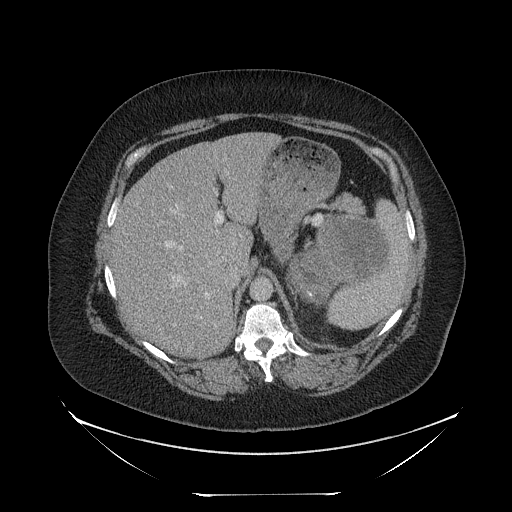
Contrast-enhanced abdominal CT, one axial slice. Position 163 of 205 along the scan axis. Reconstruction kernel STANDARD. 120 kVp. Intravenous contrast given. Soft-tissue window (W 400 / L 40 HU). 2.5 mm slice thickness. 512 × 512 image matrix. Female patient, age 53 years. Case-level facts recorded for this patient, not image findings: diagnosis: adrenocortical carcinoma; tumour side: left adrenal; tumour size at pathology: 17 cm; Ki-67 index: 20 %; stage (as recorded): 3.
Annotated regions visible in this slice (semi-automatically segmented with operator editing):
- mass: bounding box [x1, y1, x2, y2] px = [291, 222, 384, 302]